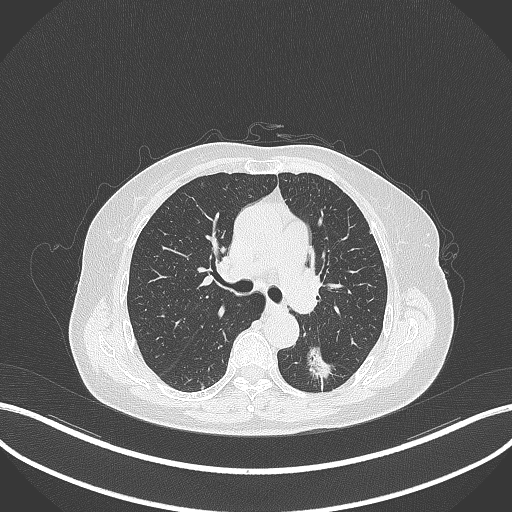
Chest CT, one axial slice. Position 185 of 352 along the scan axis. 120 kVp. Lung window (W 1500 / L -600 HU). 1 mm slice thickness. 512 × 512 image matrix, field of view 400 × 400 mm. Patient: female, 70 years. Case-level facts recorded for this patient, not image findings: clinical TNM (as recorded): T1c N0 M0.
Annotated regions visible in this slice (bounding box drawn by a radiologist):
- lung tumour (recorded histology: adenocarcinoma): bounding box [x1, y1, x2, y2] px = [305, 342, 337, 384]